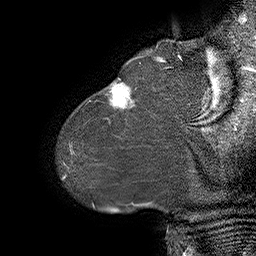
Breast MRI (dynamic contrast-enhanced), one sagittal slice; position 6 of 55 along the scan axis; dynamic contrast-enhanced series, time point 2 of 6 at this slice position (early post-contrast); 1.5 T; TE 4.5 ms, TR 32.4 ms; 3 mm slice thickness; 256 × 256 image matrix. Female patient. Case-level facts recorded for this patient, not image findings: setting: breast cancer imaged before/during neoadjuvant chemotherapy; receptor status: HER2-positive.
Structures marked on this image (semi-automatic segmentation, software-assisted and operator-edited):
- analysis volume of interest (the breast-tissue region the enhancement analysis was run in; not a lesion): bounding box [x1, y1, x2, y2] px = [80, 64, 163, 134]
- tumour enhancement mask (voxels above the 100 % enhancement threshold inside the analysis volume of interest): [109, 83, 134, 109]